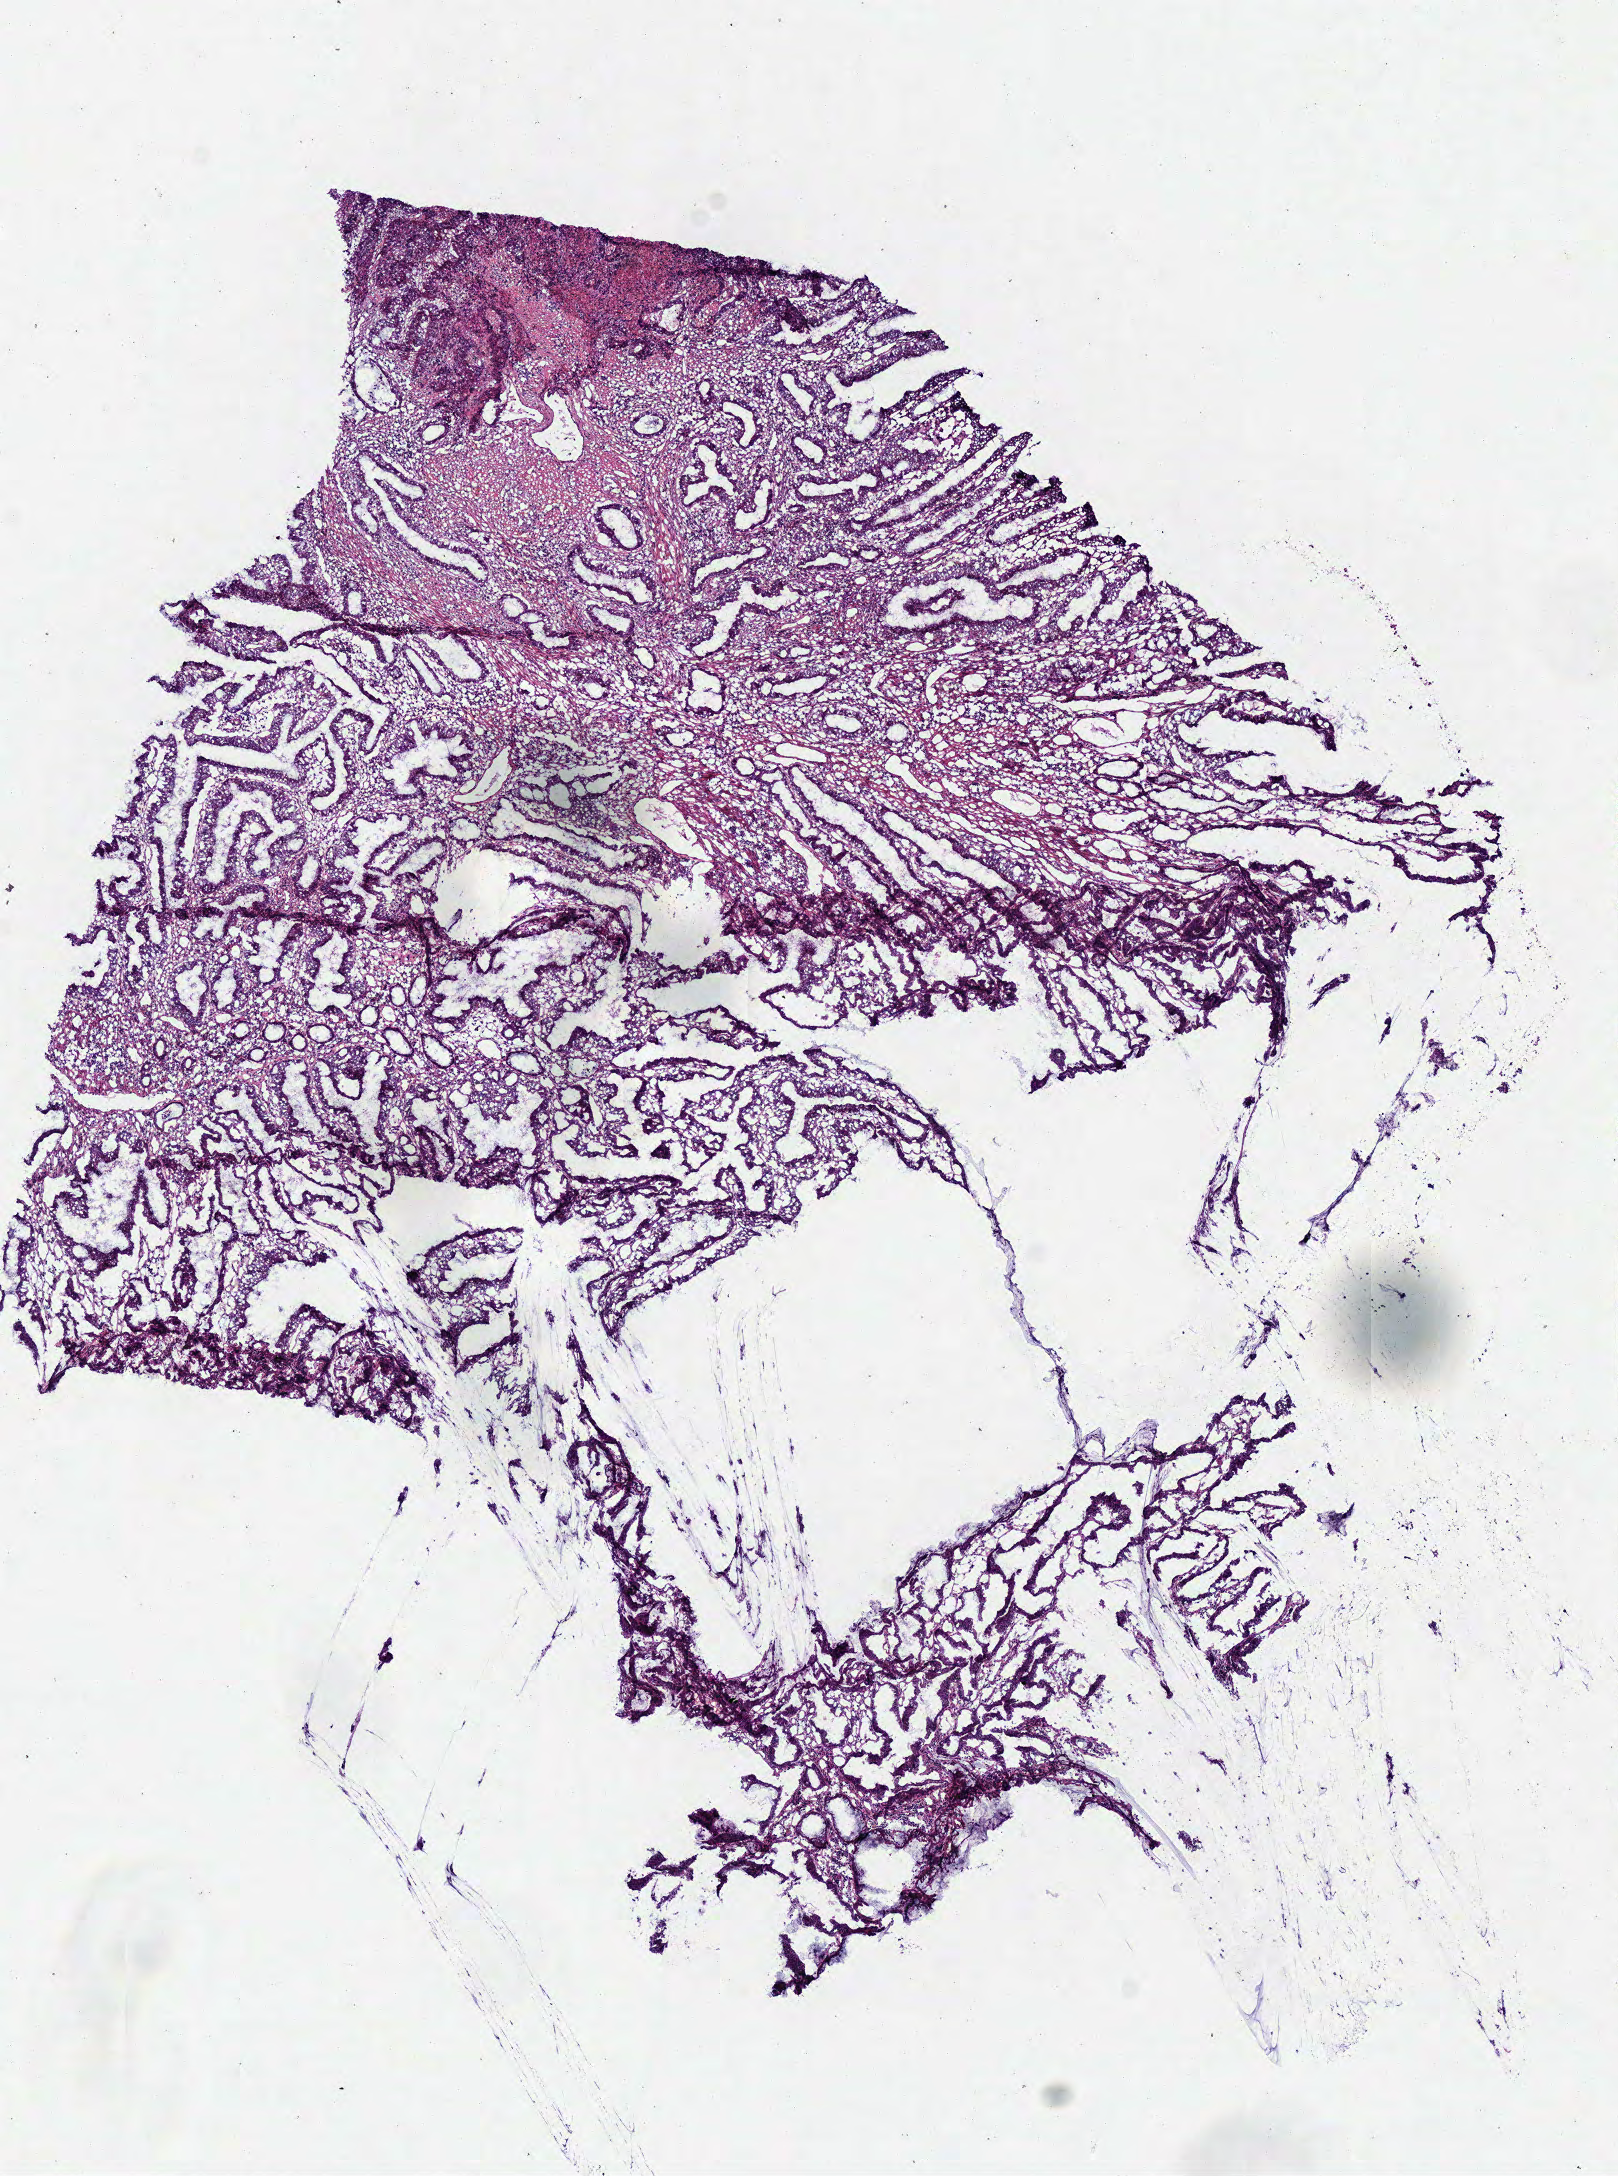
Digitized Hematoxylin and eosin (H&E) stained tissue section (whole slide) — whole scanned area (about 6.4 x 8.6 mm, slide scanned at 40x) shown as a low-resolution overview, frozen section, primary tumour sample from the colon. Patient: male, age at initial diagnosis 65 years.
Diagnosis: Mucinous adenocarcinoma (descending colon).